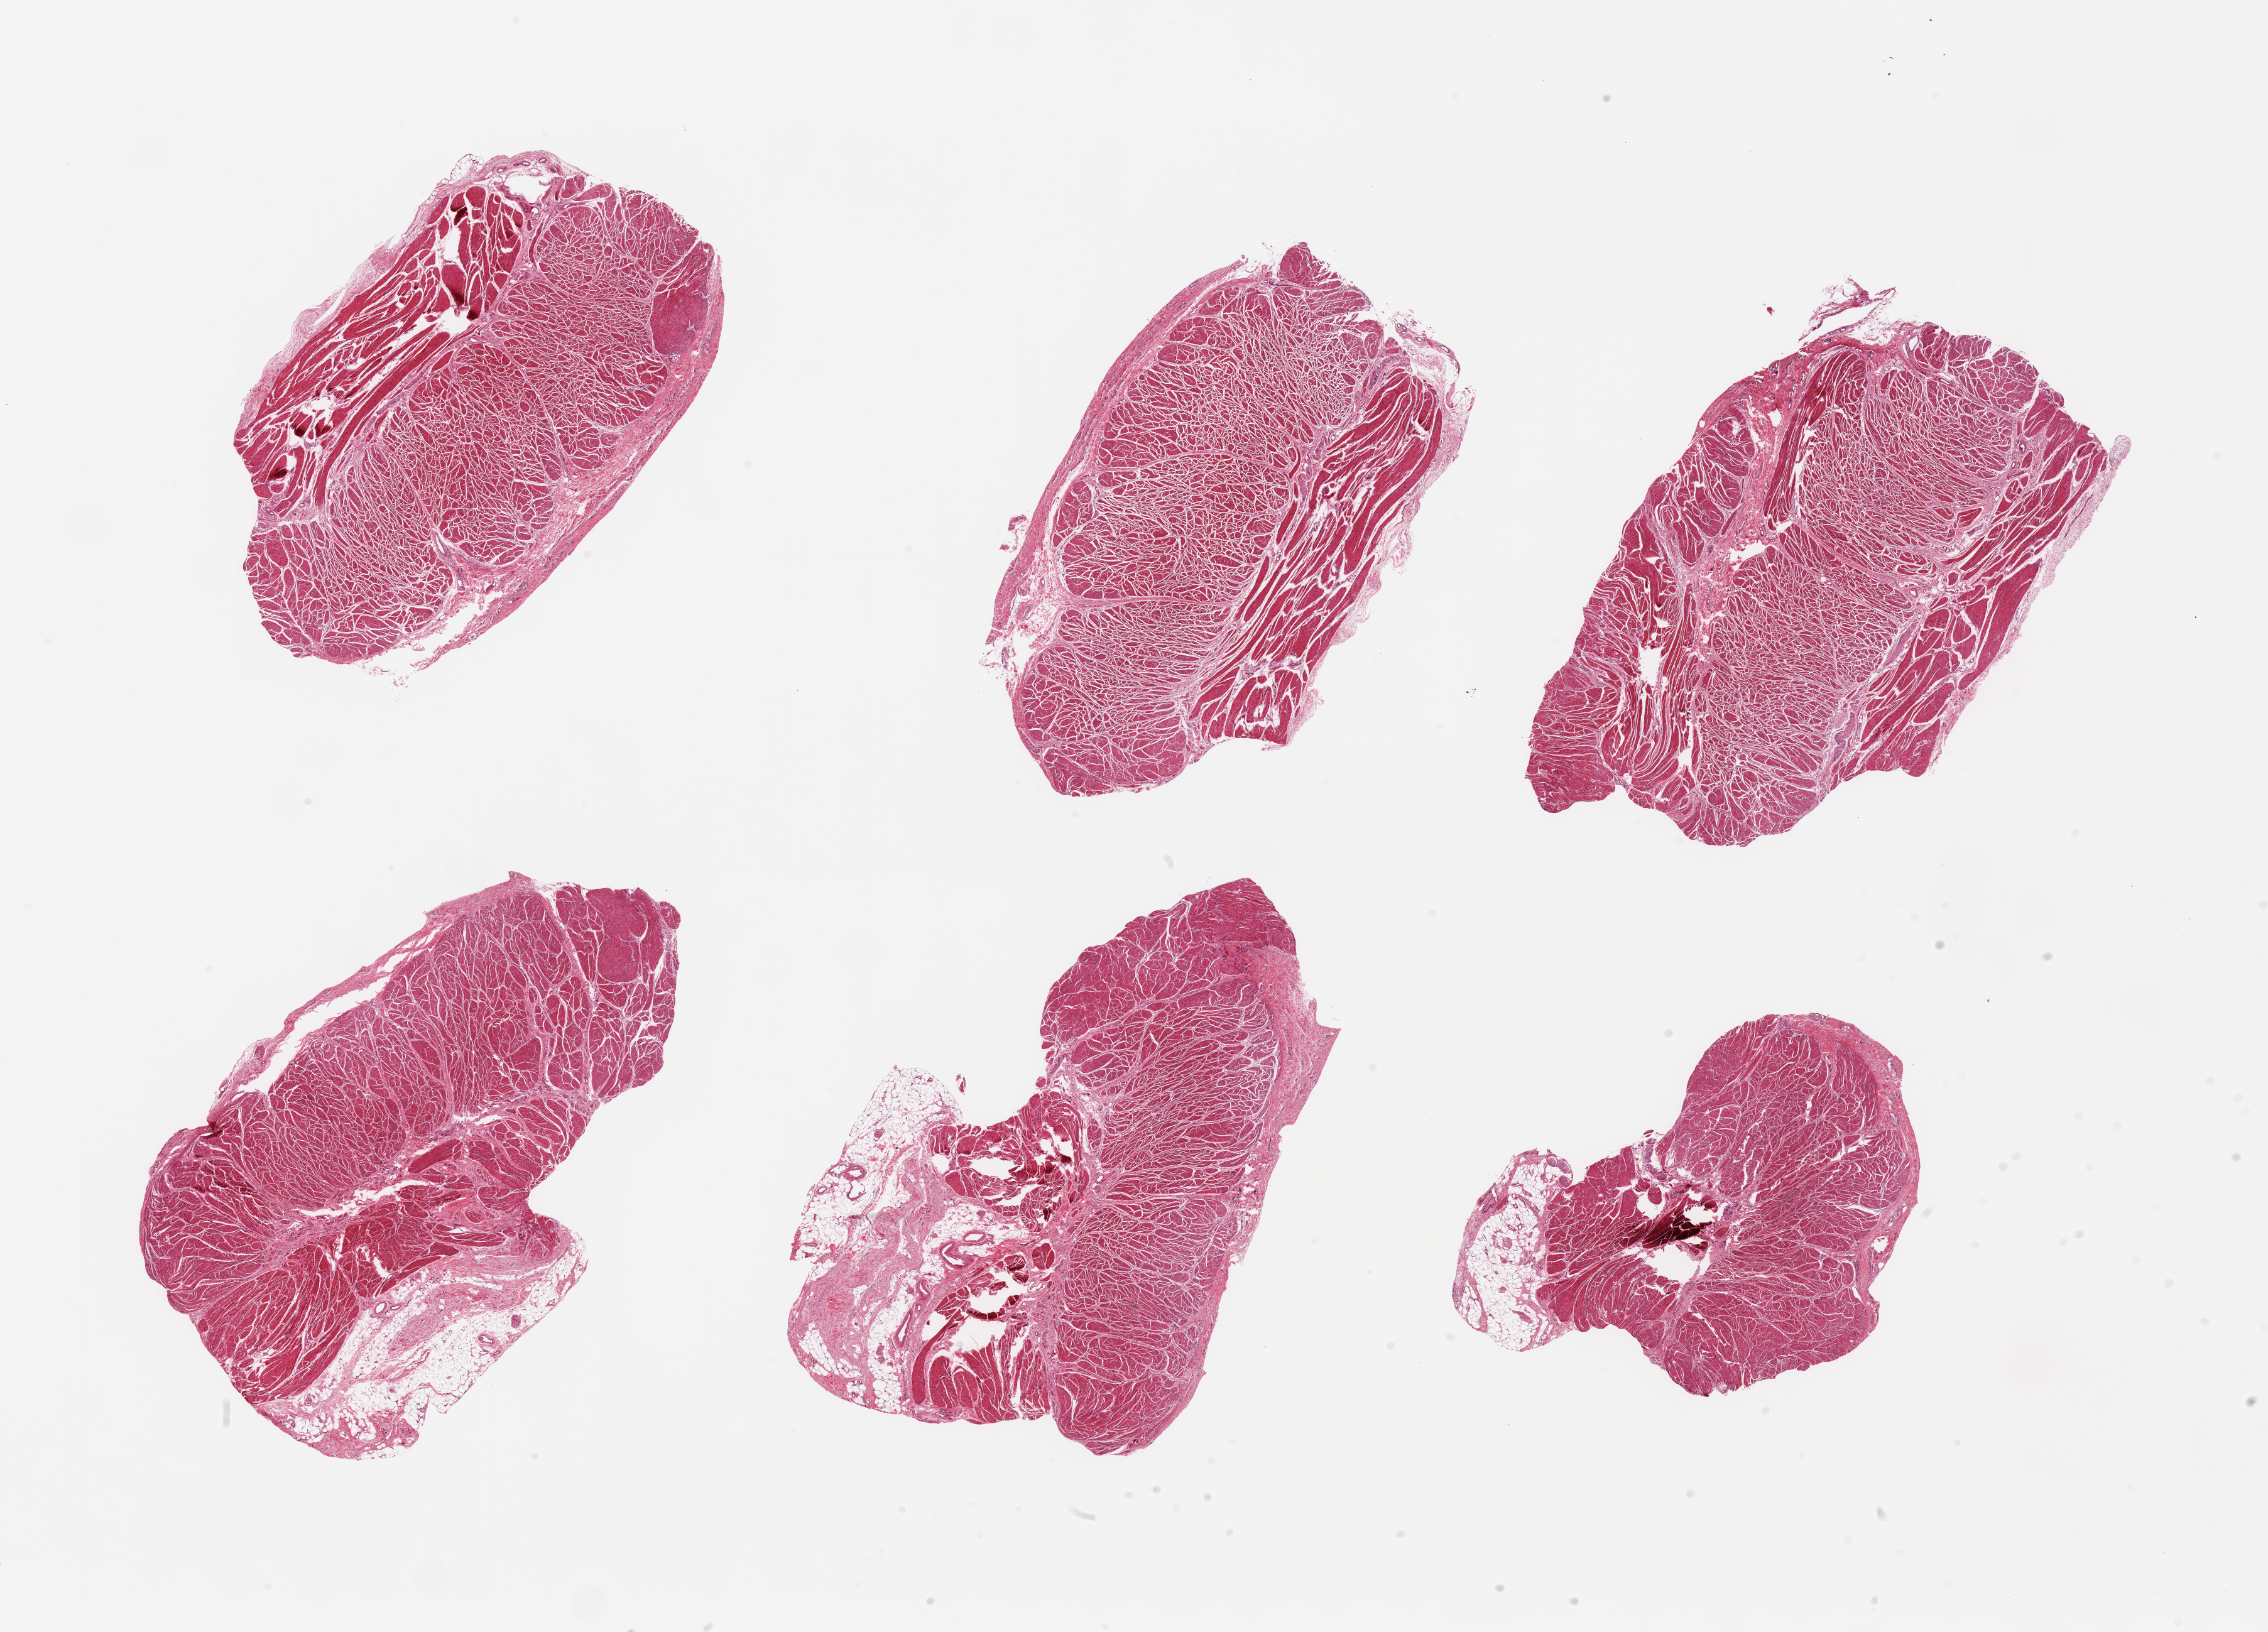
Digitized hematoxylin and eosin (H&E)-stained section, shown as a low-resolution overview of the whole scanned area (about 28.5 x 20.5 mm), PAXgene-fixed, paraffin-embedded tissue, target tissue: gastroesophageal junction, donor tissue sample.
• review note (as recorded): 6 pieces; 3 pieces well trimmed; 3 pieces with up to 2.5mm perimuscular stroma